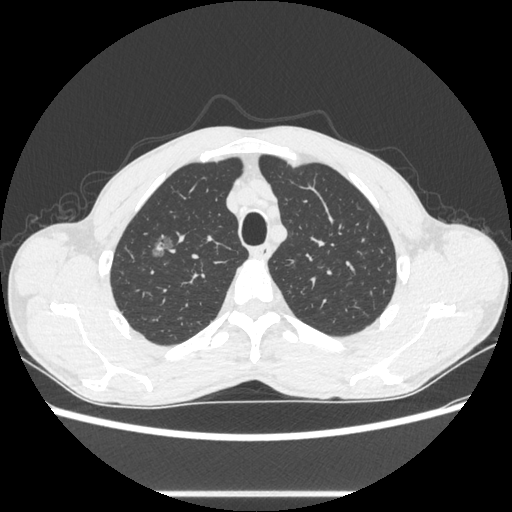
Chest CT, one axial slice. Position 481 of 600 along the scan axis. Reconstruction kernel STANDARD. Lung window (W 1500 / L -600 HU). 512 × 512 image matrix. Male patient, age 54 years. Case-level facts recorded for this patient, not image findings: clinical TNM (as recorded): T1a N0 M0.
Outlined on this slice (bounding box drawn by a radiologist):
- lung tumour (recorded histology: adenocarcinoma): bounding box [x1, y1, x2, y2] px = [144, 221, 181, 267]